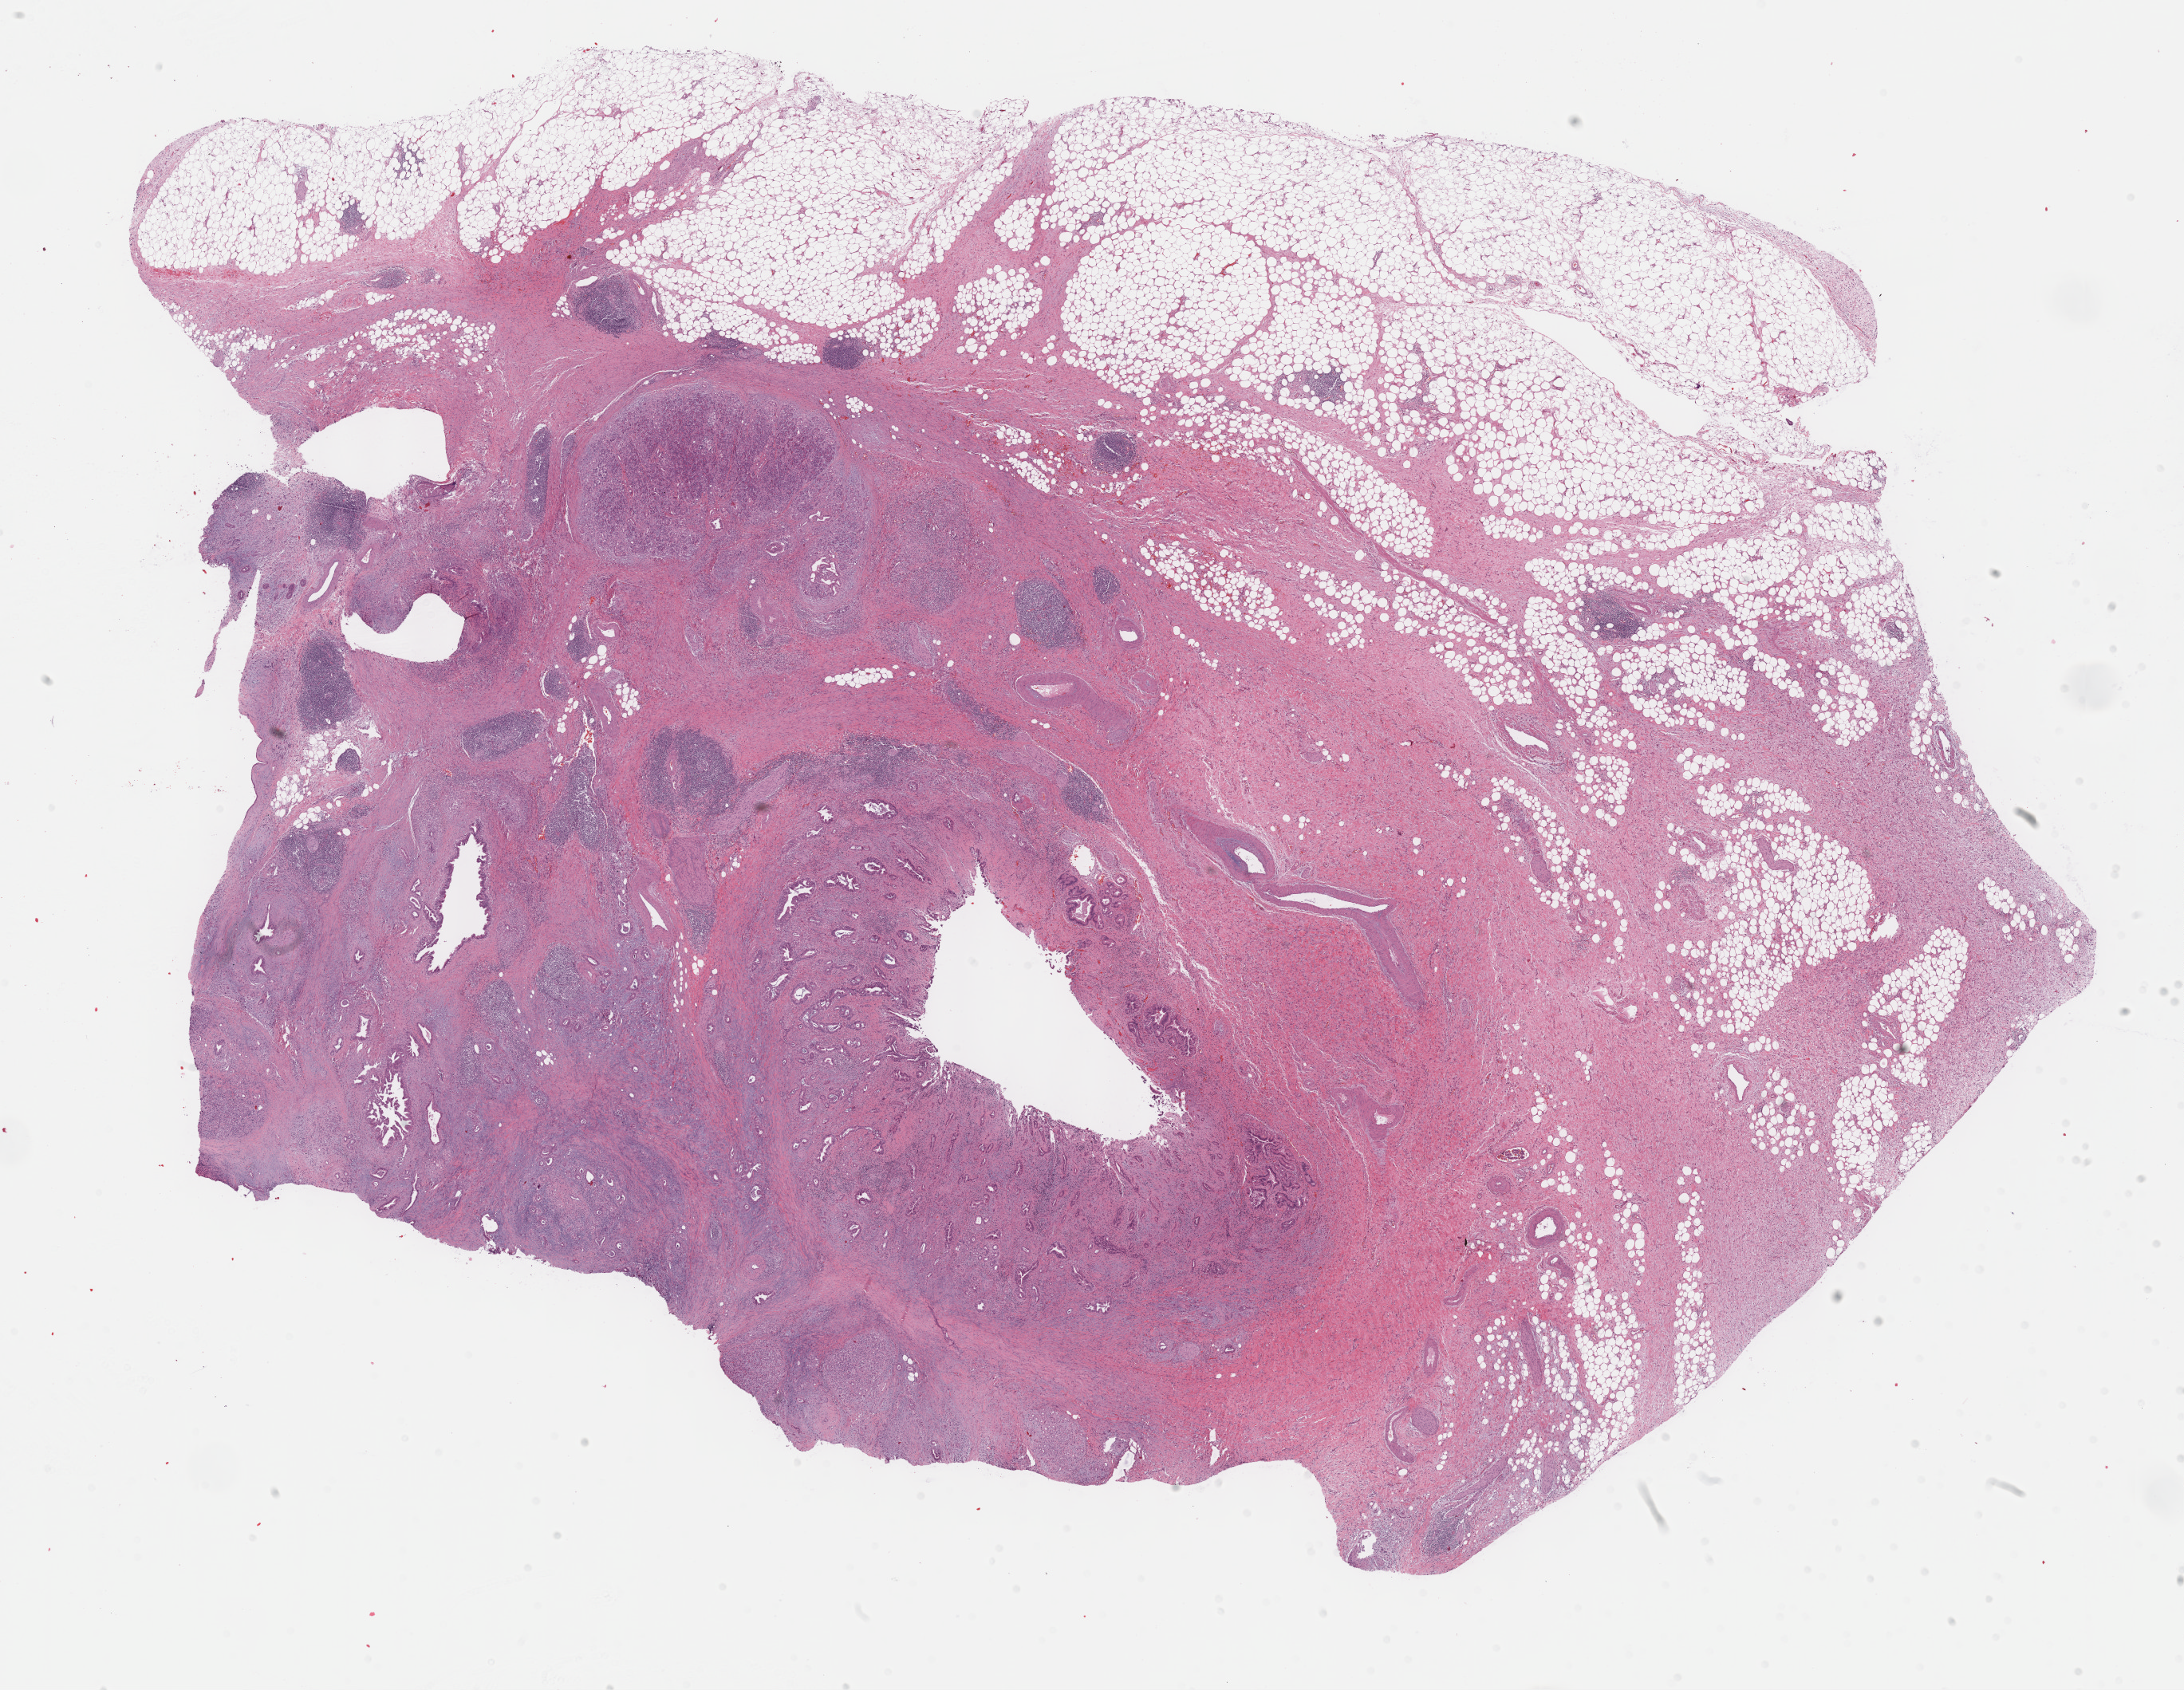
Digitized Hematoxylin and eosin (H&E) stained tissue section (whole slide) — low-resolution overview of the scanned area, about 22.1 x 17.1 mm (slide scanned at 40x), formalin-fixed paraffin-embedded (FFPE) diagnostic section, pancreas, primary tumour sample. Female, age 60 years at initial diagnosis. Histologic grade: G2 (moderately differentiated).
Diagnosis: Infiltrating duct carcinoma, NOS (head of pancreas). TNM: T2 N0 M0. AJCC pathologic stage: IB (7th edition).